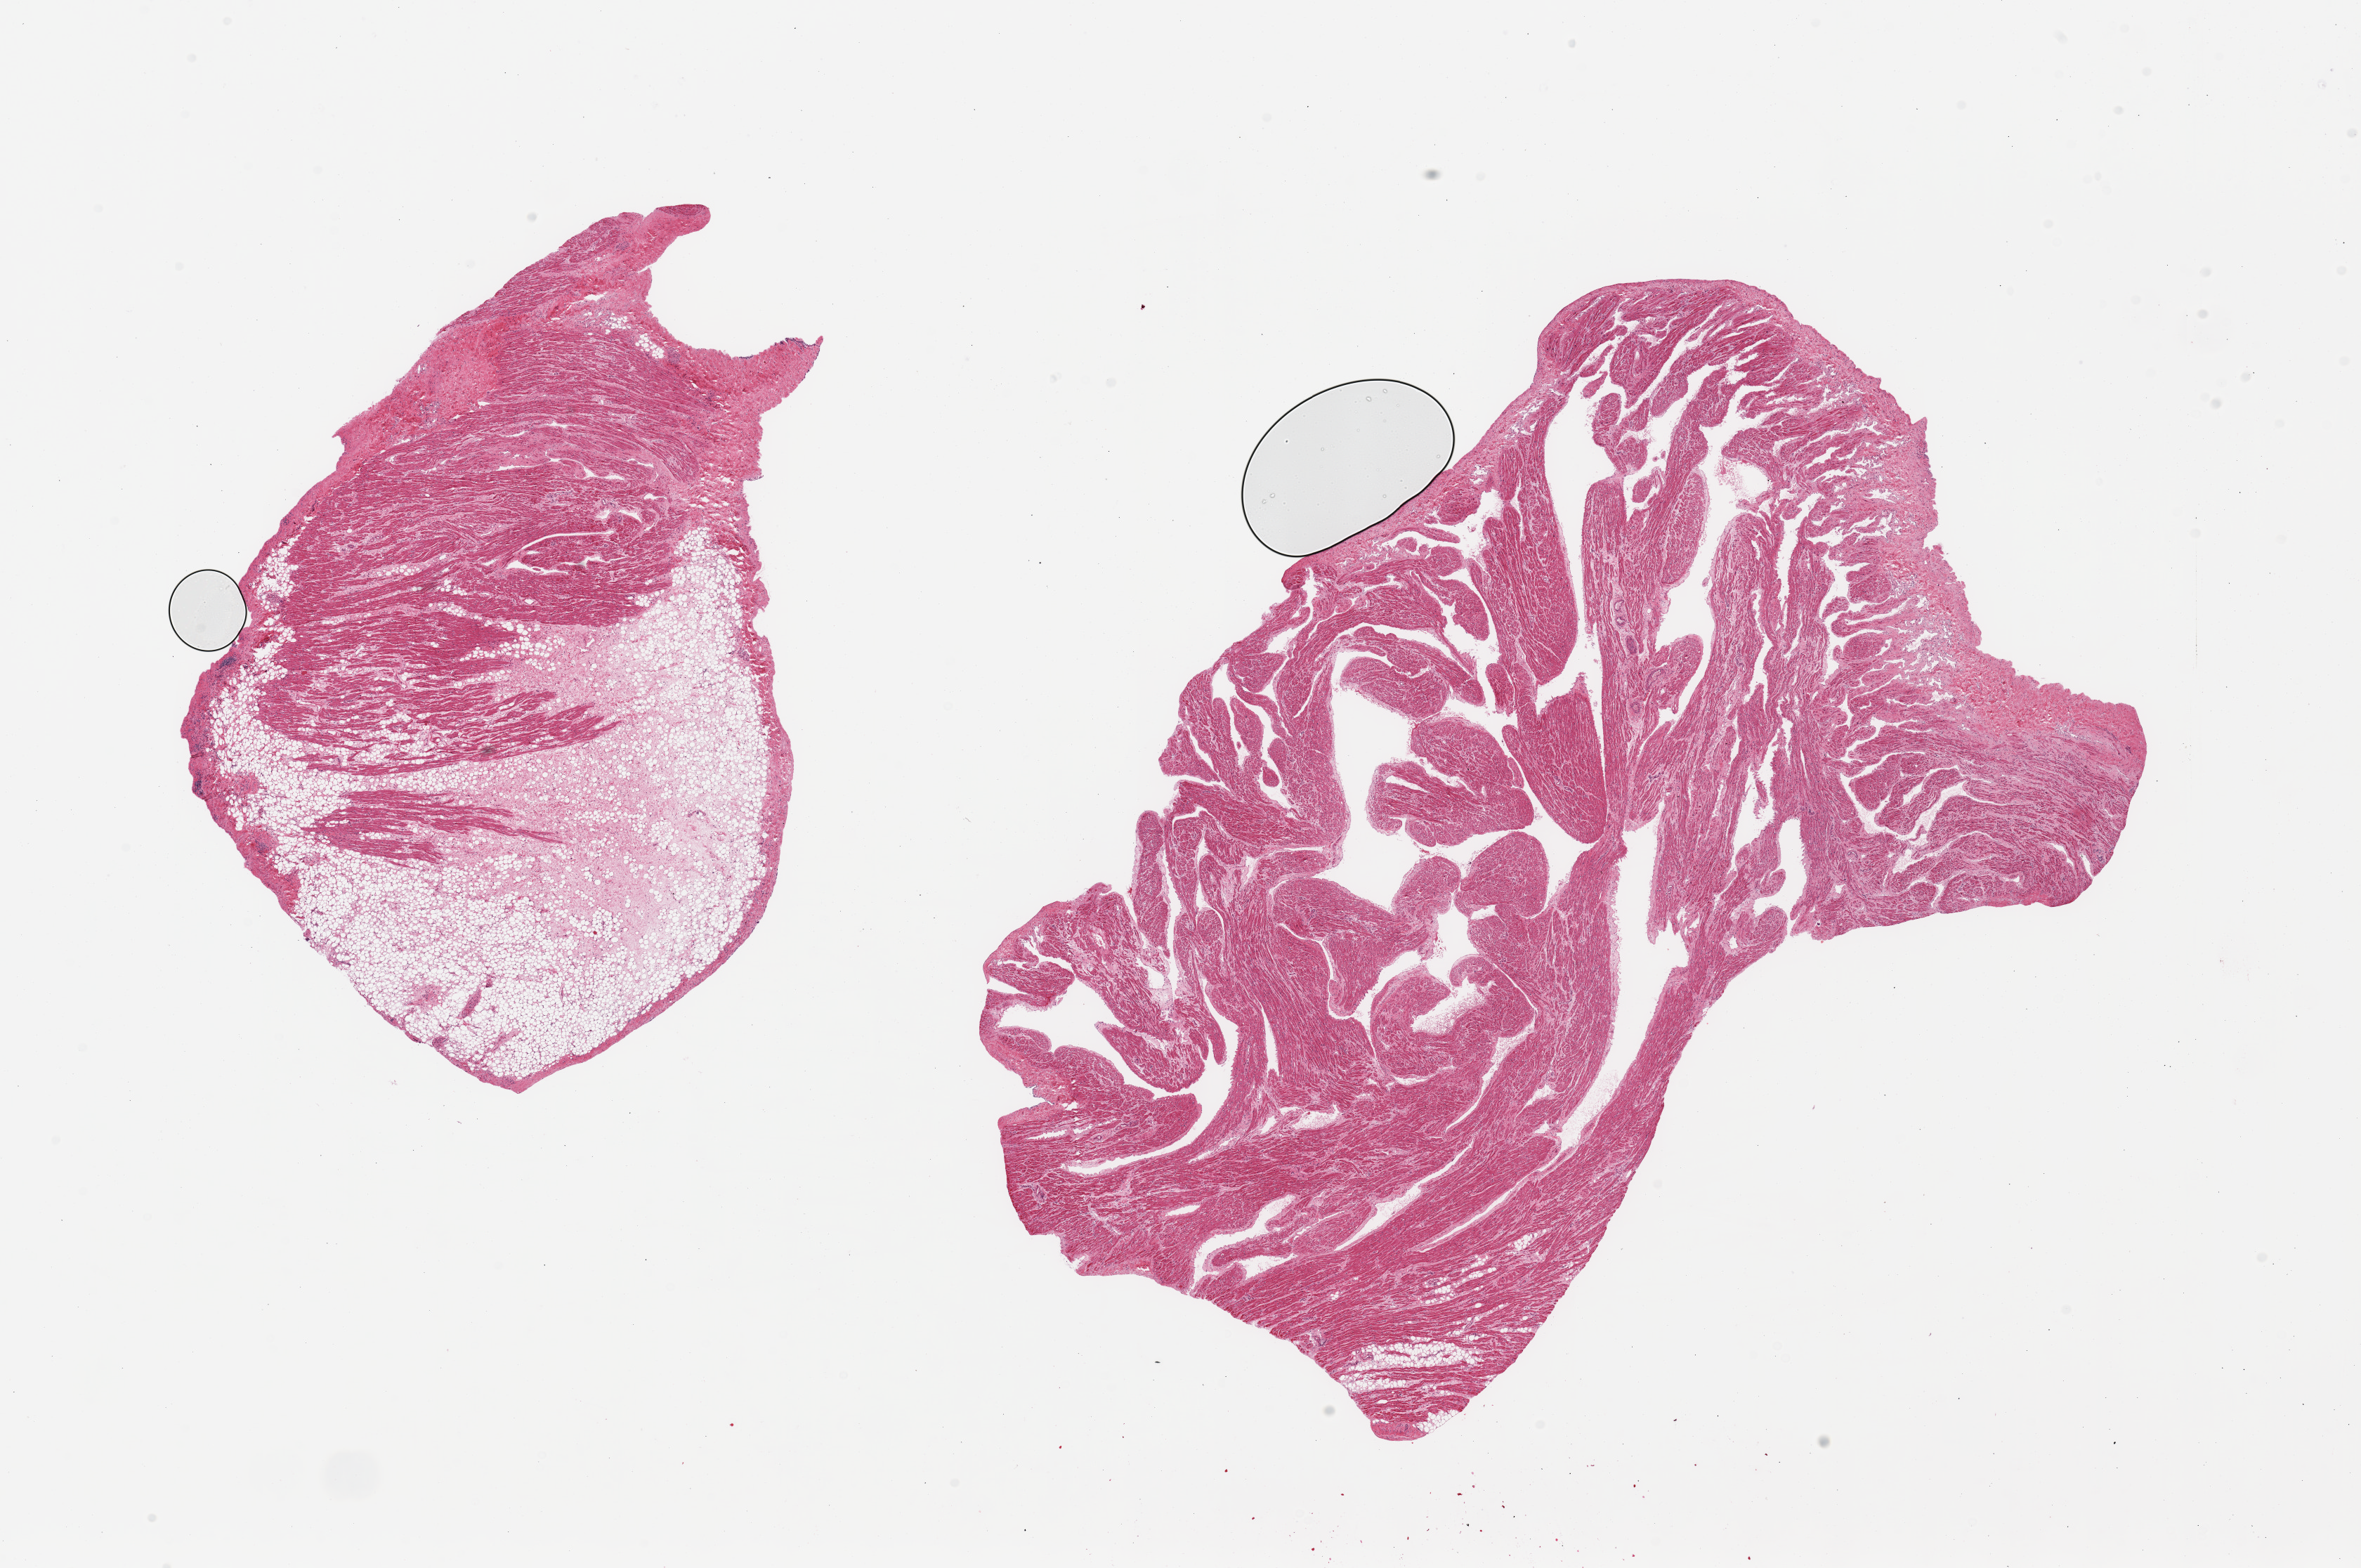
Whole-slide image, hematoxylin and eosin (H&E) stain, shown as a low-resolution overview of the whole scanned area (about 26.6 x 17.7 mm, slide scanned at 20x); PAXgene-fixed, paraffin-embedded tissue; sampled site (target tissue): auricular appendage; tissue donor sample.
* pathologist's review note for this sample: 2 pieces, no abnormalities